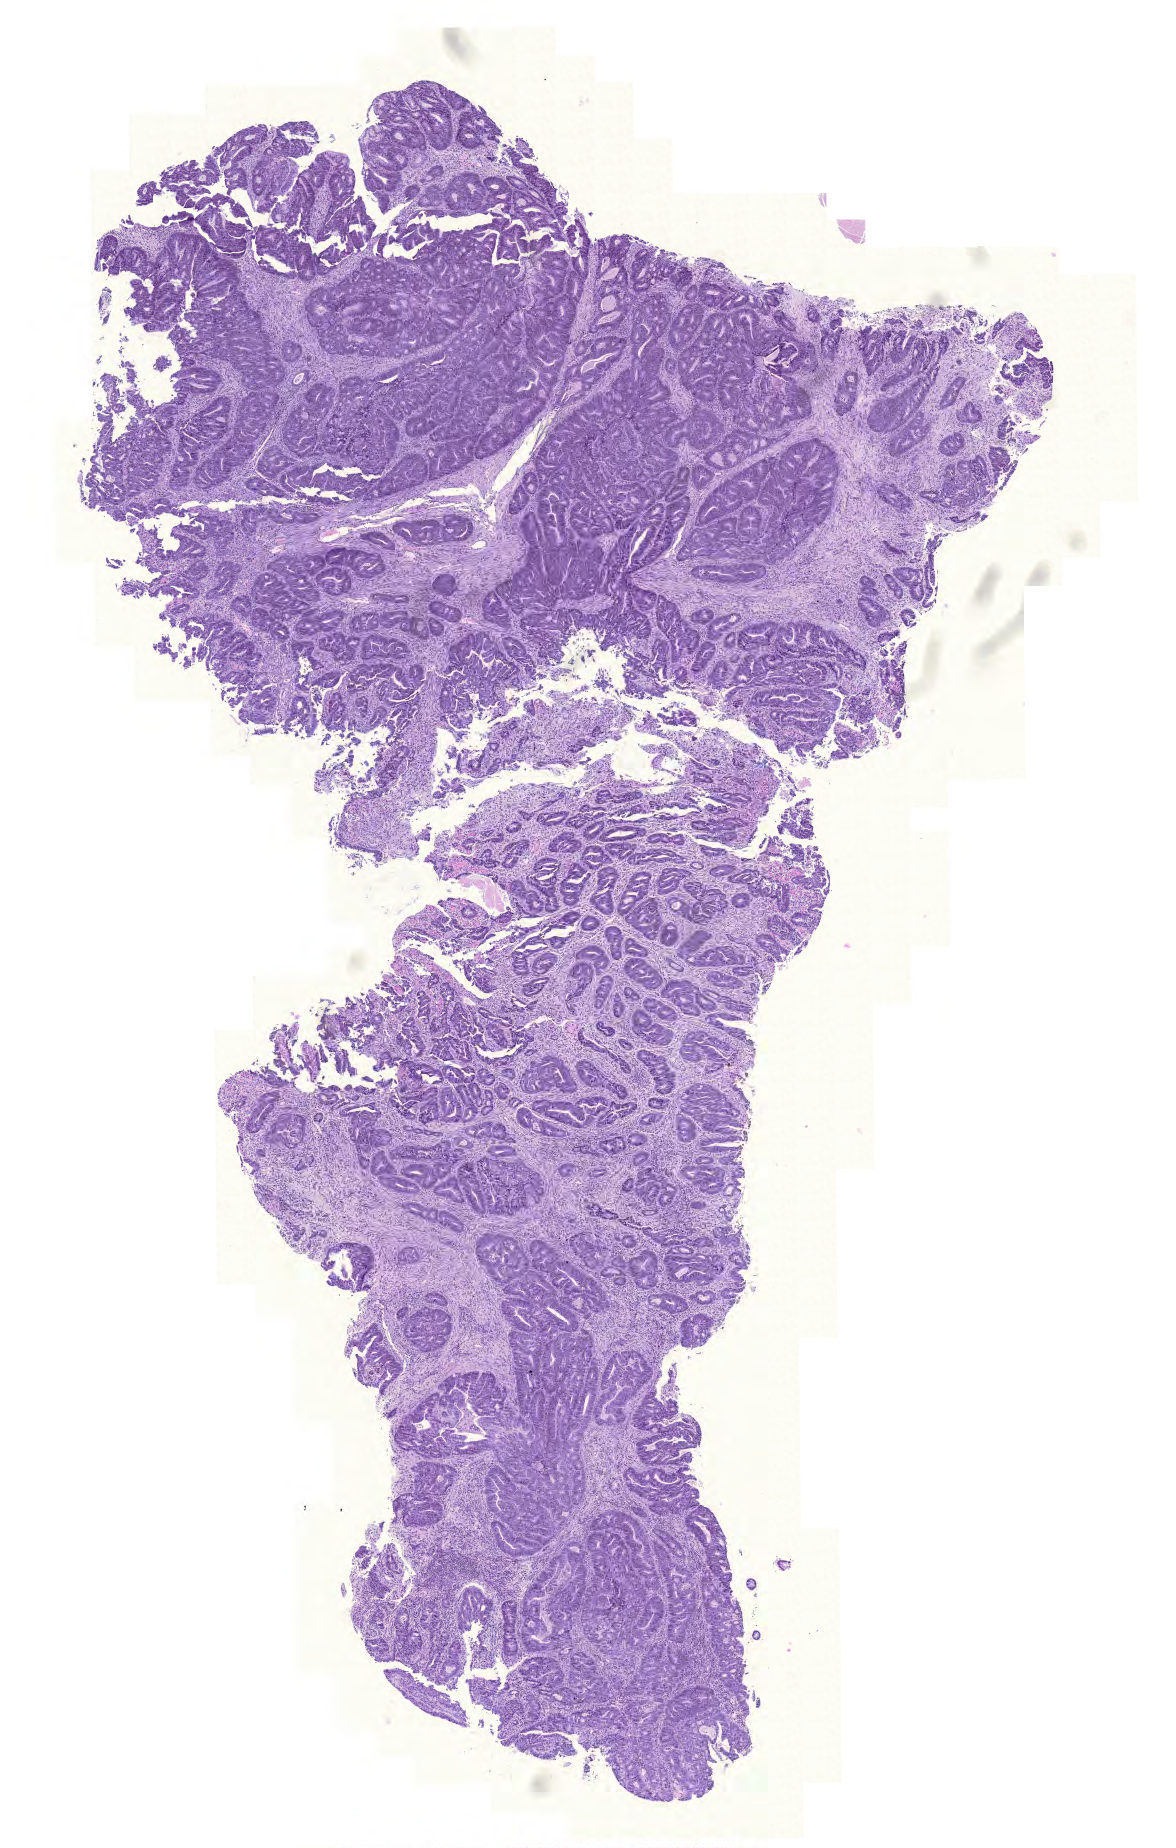
Whole-slide histology image, H&E — shown as a low-resolution overview of the whole scanned area (about 8.7 x 13.7 mm, from a 20x scan). FFPE section. Colon, primary tumour sample. Female patient; age at initial diagnosis 81 years.
• diagnosis: Adenocarcinoma, NOS
• AJCC pathologic stage: I
• TNM: T2 N0 M0